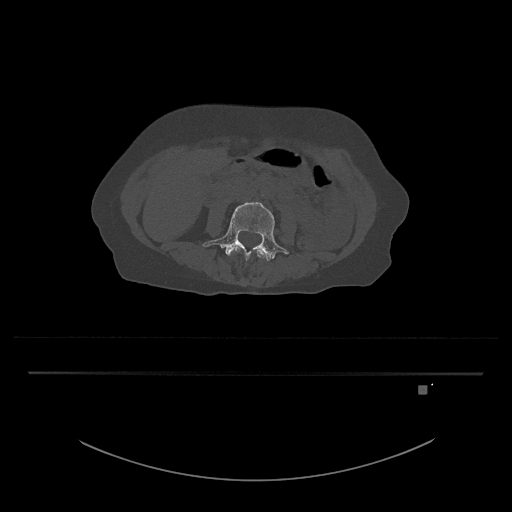
CT including the spine, one axial slice. Slice 375 of 797 in the series (ordered by position). Reconstruction kernel Br40s/3. 120 kVp. Bone window (W 1800 / L 400 HU). 512 × 512 image matrix, field of view 500 × 500 mm. Female patient, age 57 years. Case-level facts recorded for this patient, not image findings: primary cancer: cervical.
Structures marked on this image (semi-automatically segmented with operator editing):
- L3 vertebra: box from (x=233, y=249) to (x=266, y=259) px
- L4 vertebra: (x=202, y=202)–(x=290, y=262)